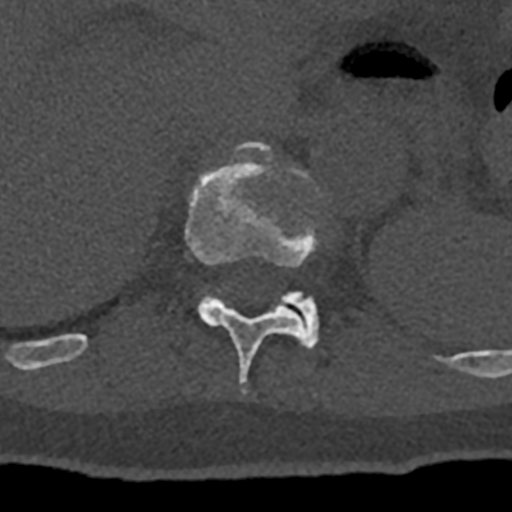
CT including the spine, one axial slice. Position 534 of 797 along the scan axis. 120 kVp. Bone window (W 1800 / L 400 HU). 512 × 512 image matrix, field of view 160 × 160 mm. Male patient, age 74 years. From the clinical record (not read from this slice): primary cancer: renal; vertebrae with lytic lesions (as recorded): T10, L1, L2, L3, L4, L5.
Outlined on this slice (semi-automatic segmentation, software-assisted and operator-edited):
- T11 vertebra: bounding box [x1, y1, x2, y2] px = [70, 141, 317, 394]
- T12 vertebra: [280, 291, 319, 350]